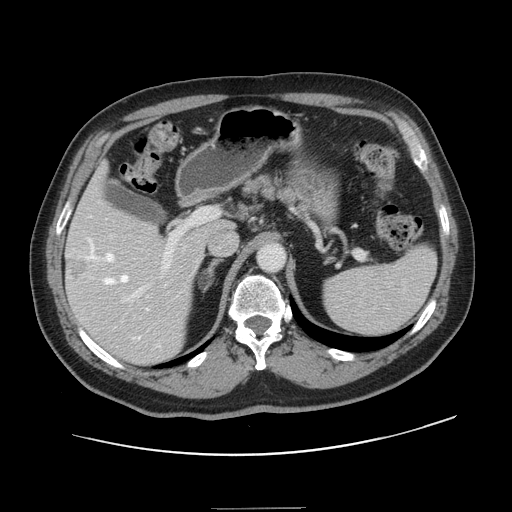
Contrast-enhanced abdominal CT, one axial slice; slice 89 of 143 in the series (ordered by position); intravenous contrast given; soft-tissue window (W 400 / L 40 HU); 2.5 mm slice thickness; 512 × 512 image matrix, field of view 402 × 402 mm. Male patient, age 62 years. Case-level facts recorded for this patient, not image findings: diagnosis: colorectal cancer liver metastases, imaged before liver resection; multiple liver metastases: yes; largest metastasis: 2.7 cm; disease in both lobes: no.
Structures marked on this image (outlined manually by an expert reader):
- hepatic veins: bounding box (x1, y1, x2, y2) in pixels: (86, 240, 148, 339)
- liver: (66, 169, 230, 363)
- planned liver remnant (the part of the liver to remain after resection): (68, 170, 230, 245)
- portal vein (with intrahepatic branches): (79, 208, 217, 340)
- liver metastasis: (68, 258, 88, 279)